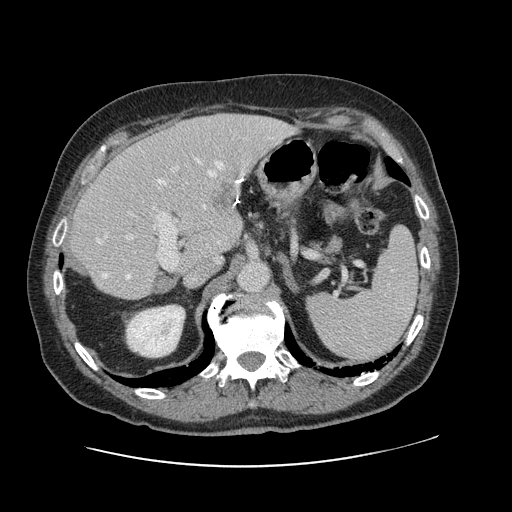
Contrast-enhanced abdominal CT, one axial slice; position 74 of 138 along the scan axis; 120 kVp; intravenous contrast given; soft-tissue window (W 400 / L 40 HU); 512 × 512 image matrix, field of view 402 × 402 mm. Male patient, age 71 years. From the clinical record (not read from this slice): diagnosis: colorectal cancer liver metastases, imaged before liver resection.
Annotated regions visible in this slice (manually delineated by an expert):
- hepatic veins: bounding box <97,159,242,279> (left, top, right, bottom; pixels)
- liver: <71,115,290,300>
- planned liver remnant (the part of the liver to remain after resection): <71,148,230,300>
- portal vein (with intrahepatic branches): <126,166,179,270>
- liver metastasis: <206,181,236,216>